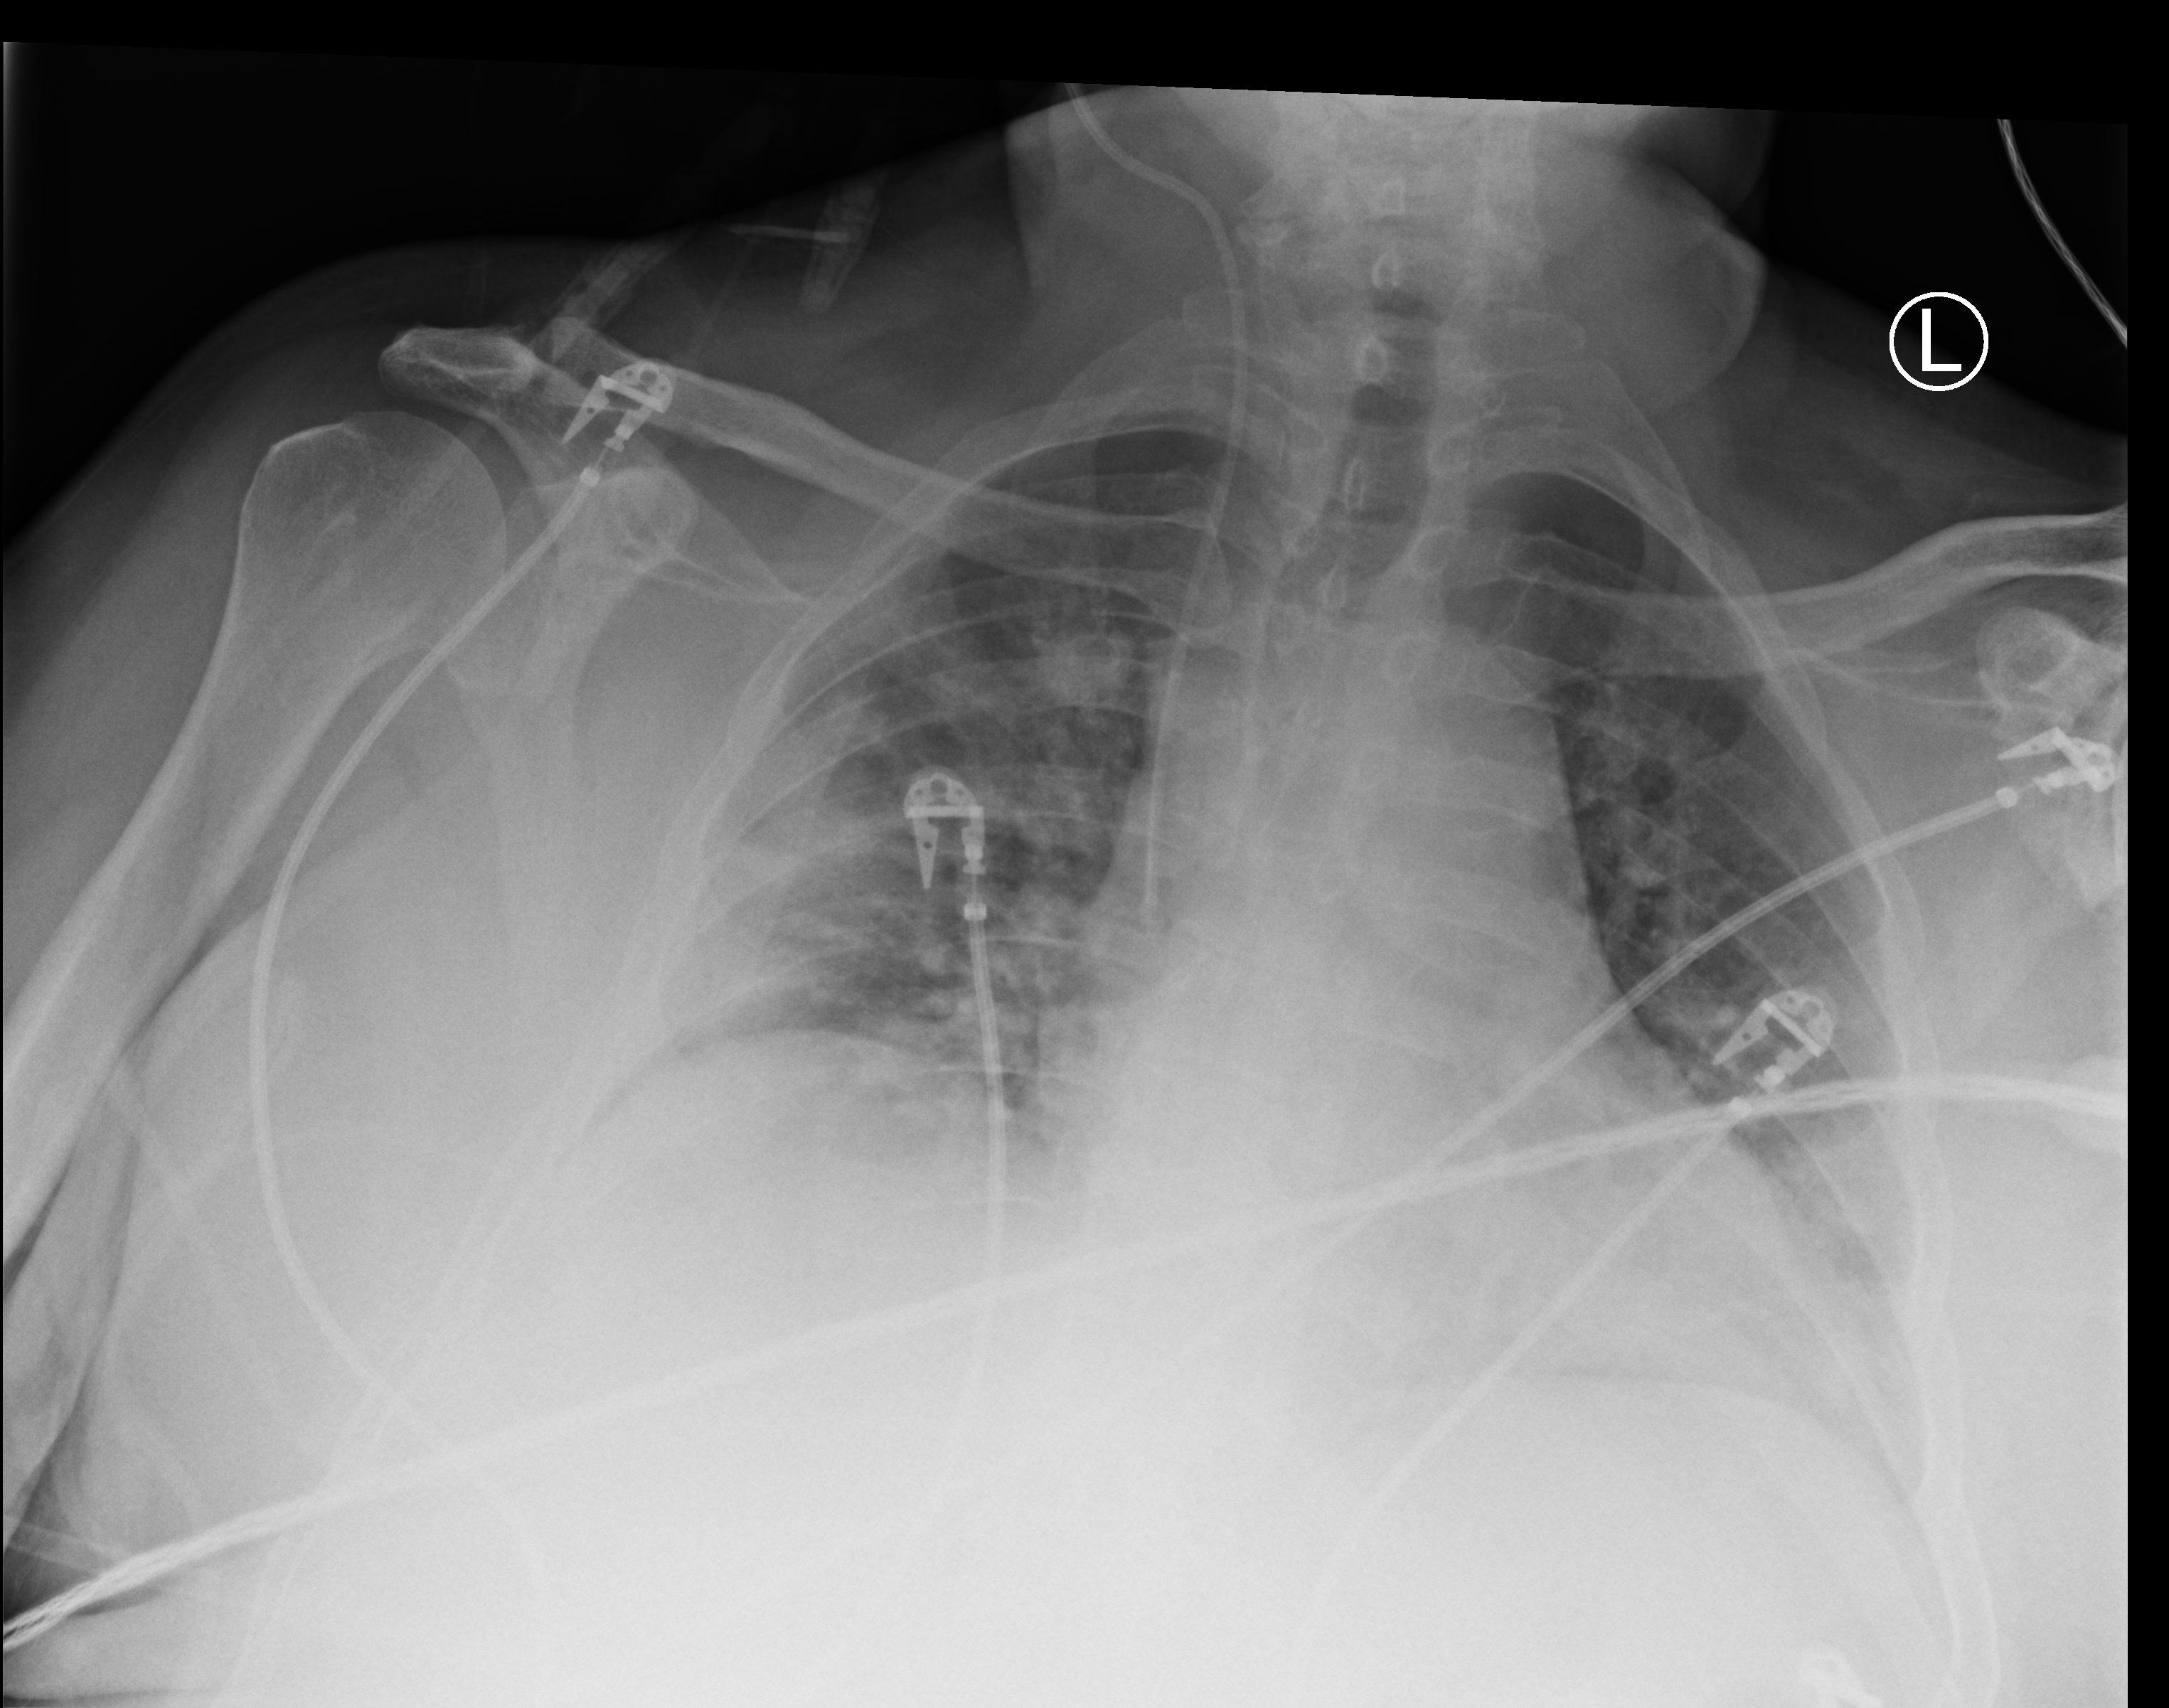
Chest X-ray (portable); anteroposterior (AP) projection. Male patient hospitalised with COVID-19, age 60–74 years.
Admission-level facts for this patient (not findings on this image; timing relative to this image not recorded): COPD (admission record): no; admitted to intensive care during this hospital stay: yes; mechanically ventilated during this hospital stay: no.